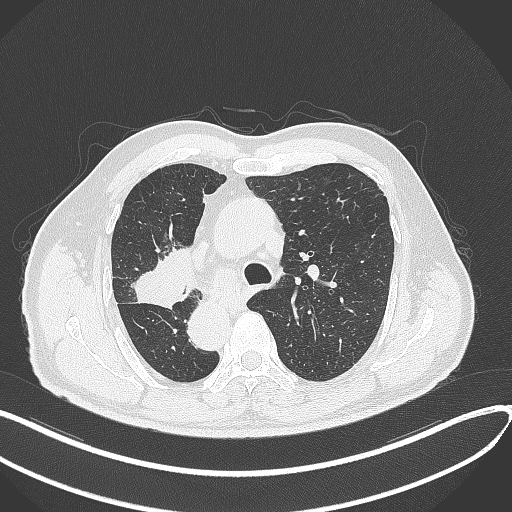
Chest CT, one axial slice; slice 211 of 300 in the series (ordered by position); 120 kVp; lung window (W 1500 / L -600 HU); 1 mm slice thickness; 512 × 512 image matrix, field of view 400 × 400 mm. Patient: male, 67 years. From the clinical record (not read from this slice): clinical TNM (as recorded): T2a N0 M0.
Structures marked on this image (bounding box drawn by a radiologist):
- lung tumour (recorded histology: squamous cell carcinoma): bounding box [x1, y1, x2, y2] px = [130, 249, 192, 311]